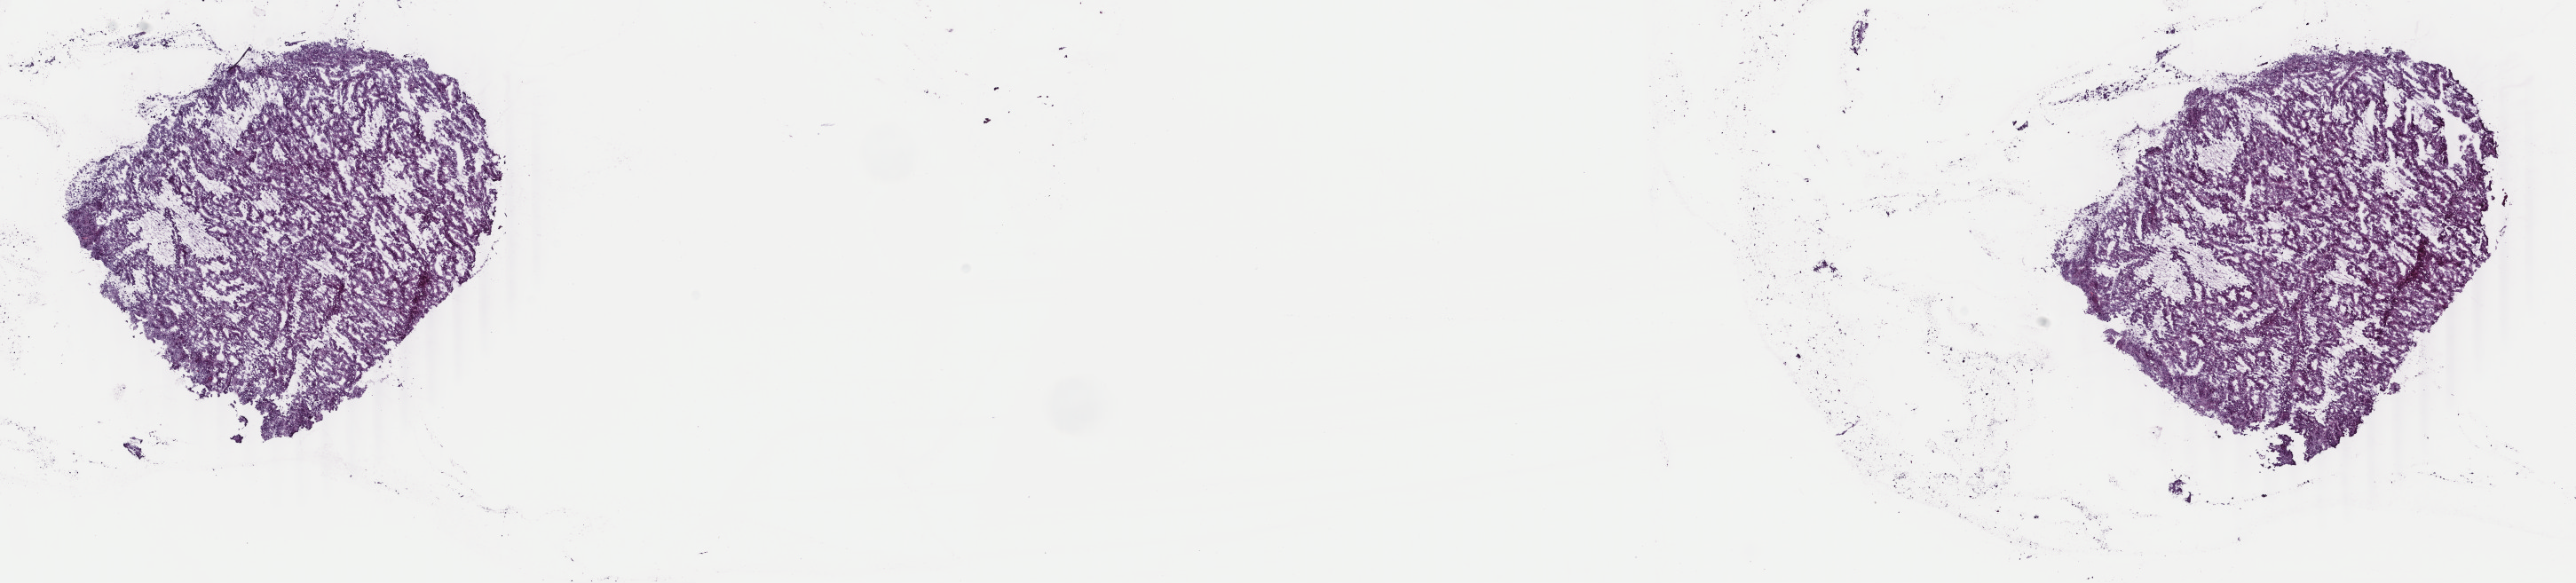
Digitized H&E tissue section (whole slide), a low-resolution overview of the entire scanned area, about 23.1 x 5.2 mm (acquisition: 40x scan), frozen section, adrenal cortex, primary tumour sample. Female patient; age at initial diagnosis 34 years. Composition of this section per pathologist review: tumour cells 100%, tumour nuclei 95%, normal cells 0%, stromal cells 0%, necrosis 0%. Inflammatory infiltration, as recorded: lymphocyte infiltration 0%, monocyte infiltration 0%, neutrophil infiltration 0%.
- histologic diagnosis: Adrenal cortical carcinoma (cortex of adrenal gland)